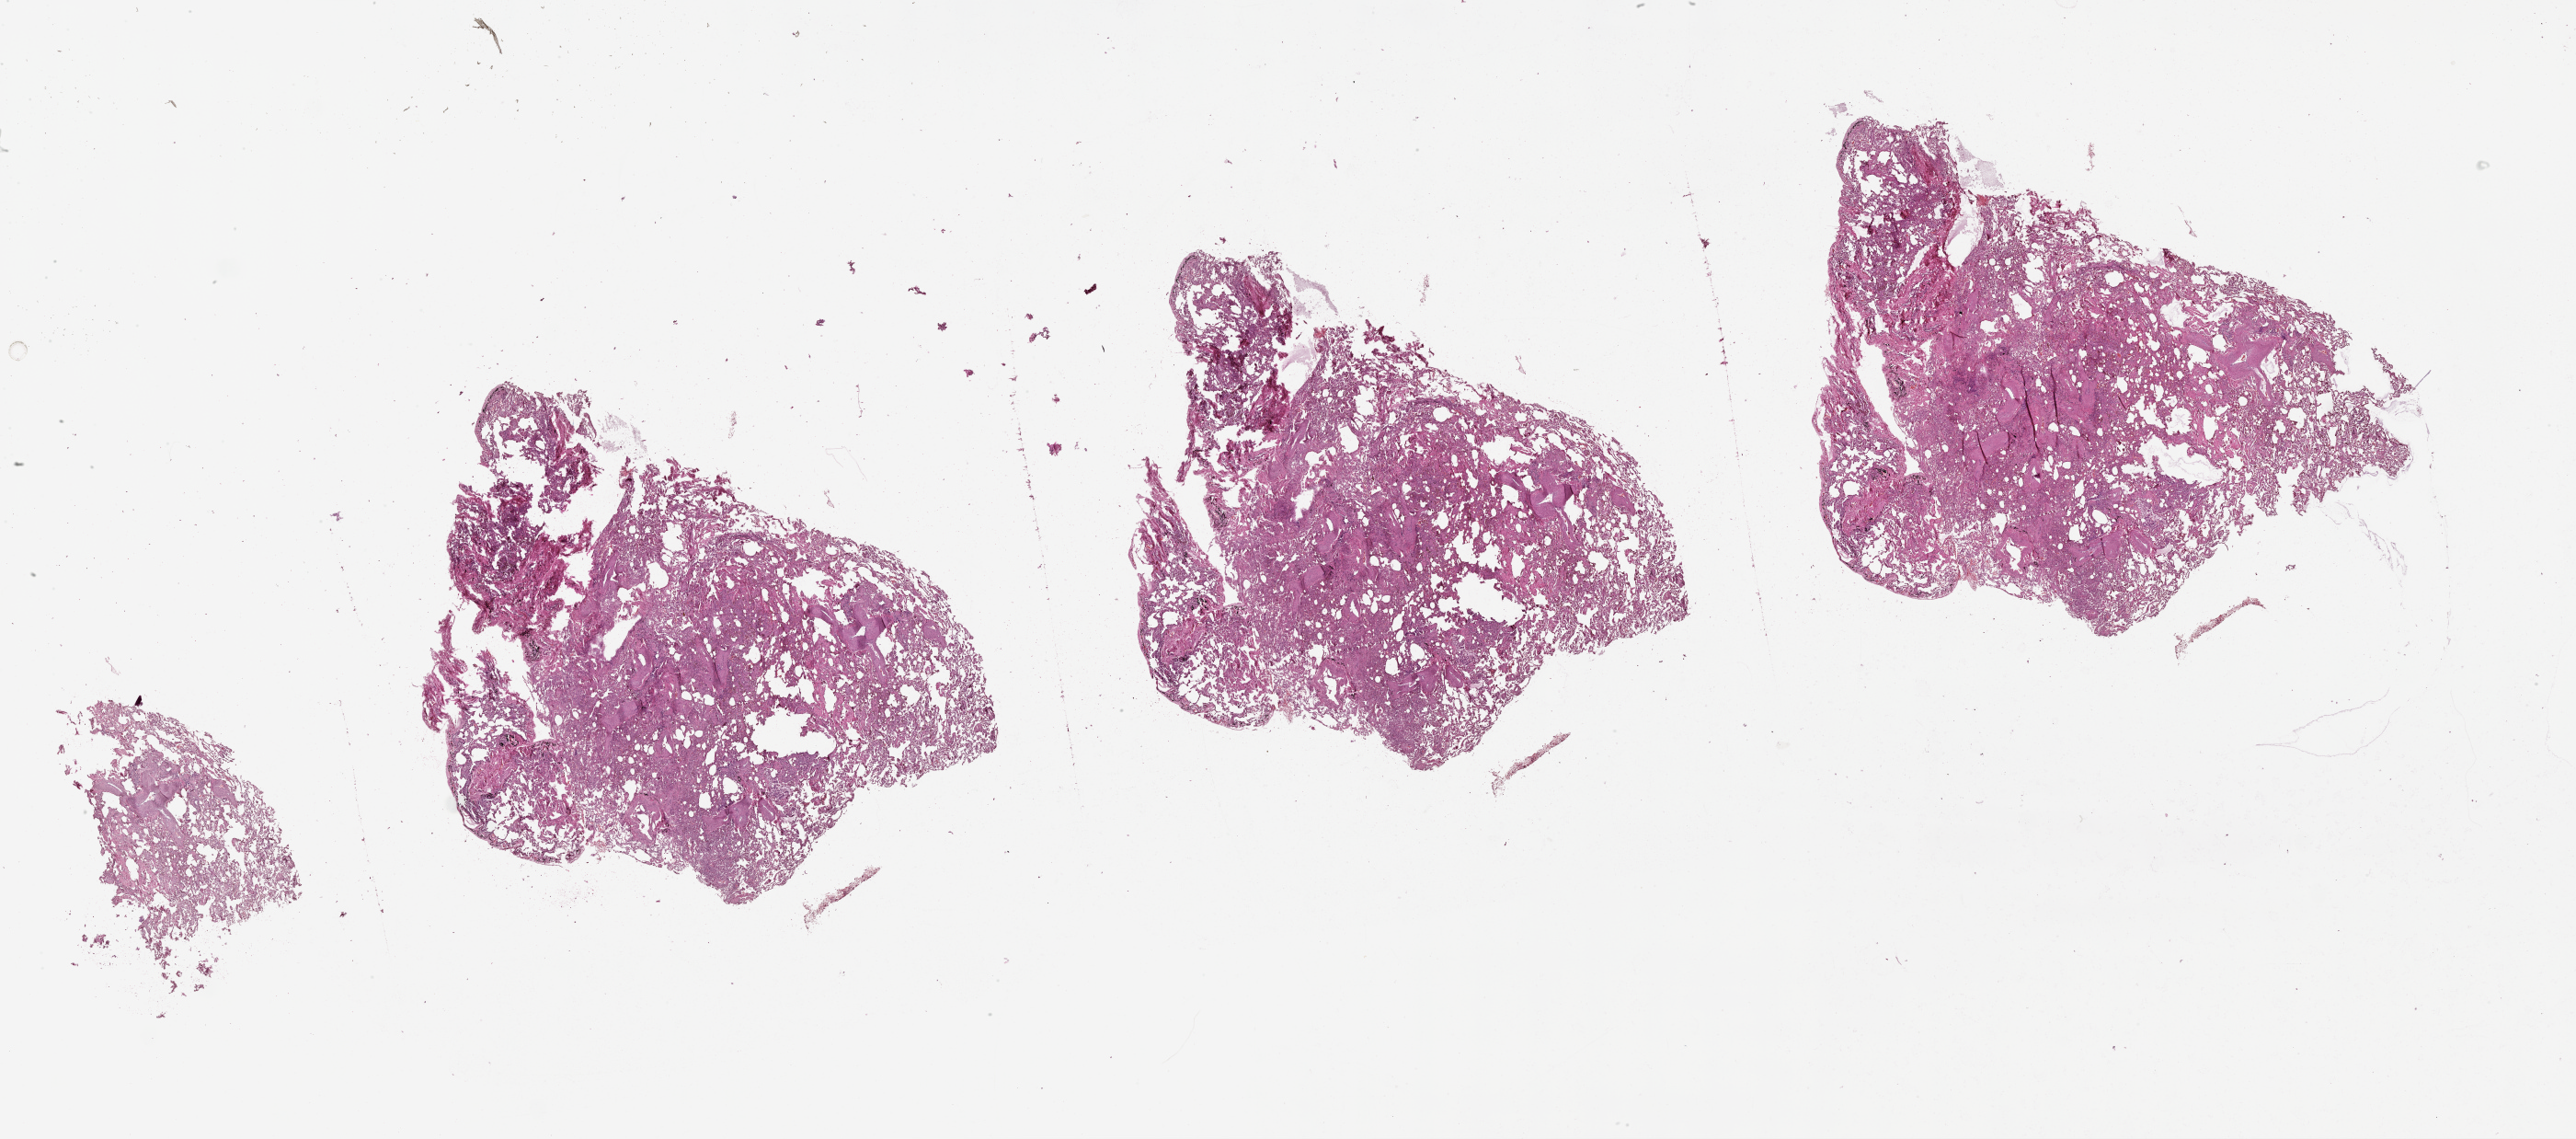
H&E-stained whole-slide image — whole scanned area (about 45.1 x 19.9 mm) shown as a low-resolution overview, lung, normal (non-tumour) tissue. Male, 63 y/o.
* this section: normal (non-tumour) tissue from the same patient
* patient diagnosis (cohort enrolment): squamous cell carcinoma (lung)